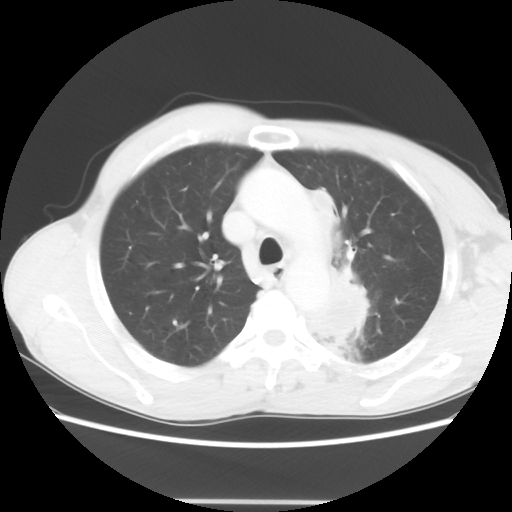
Chest CT, one axial slice; slice 47 of 62 in the series (ordered by position); reconstruction kernel STANDARD; 100 kVp; lung window (W 1500 / L -600 HU); 5 mm slice thickness; 512 × 512 image matrix. Male patient, age 61 years. From the clinical record (not read from this slice): clinical TNM (as recorded): T3 N1 M1.
Outlined on this slice (rectangle marked by the reading radiologist):
- lung tumour (recorded histology: adenocarcinoma): bounding box (x1, y1, x2, y2) in pixels: (309, 187, 375, 345)